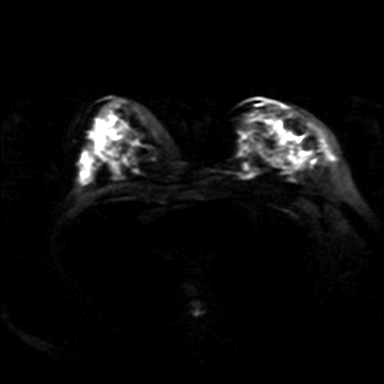
Breast MRI, one axial slice. Position 24 of 36 along the scan axis. Diffusion-weighted series; image 2 of 4 stored at this slice position (different b-values; order by instance number). 3 T. 4 mm slice thickness. 384 × 384 image matrix, field of view 320 × 320 mm. Female patient.
Outlined on this slice (outlined manually by an expert reader):
- tumour on diffusion-weighted imaging: bounding box [x1, y1, x2, y2] px = [244, 124, 295, 171]